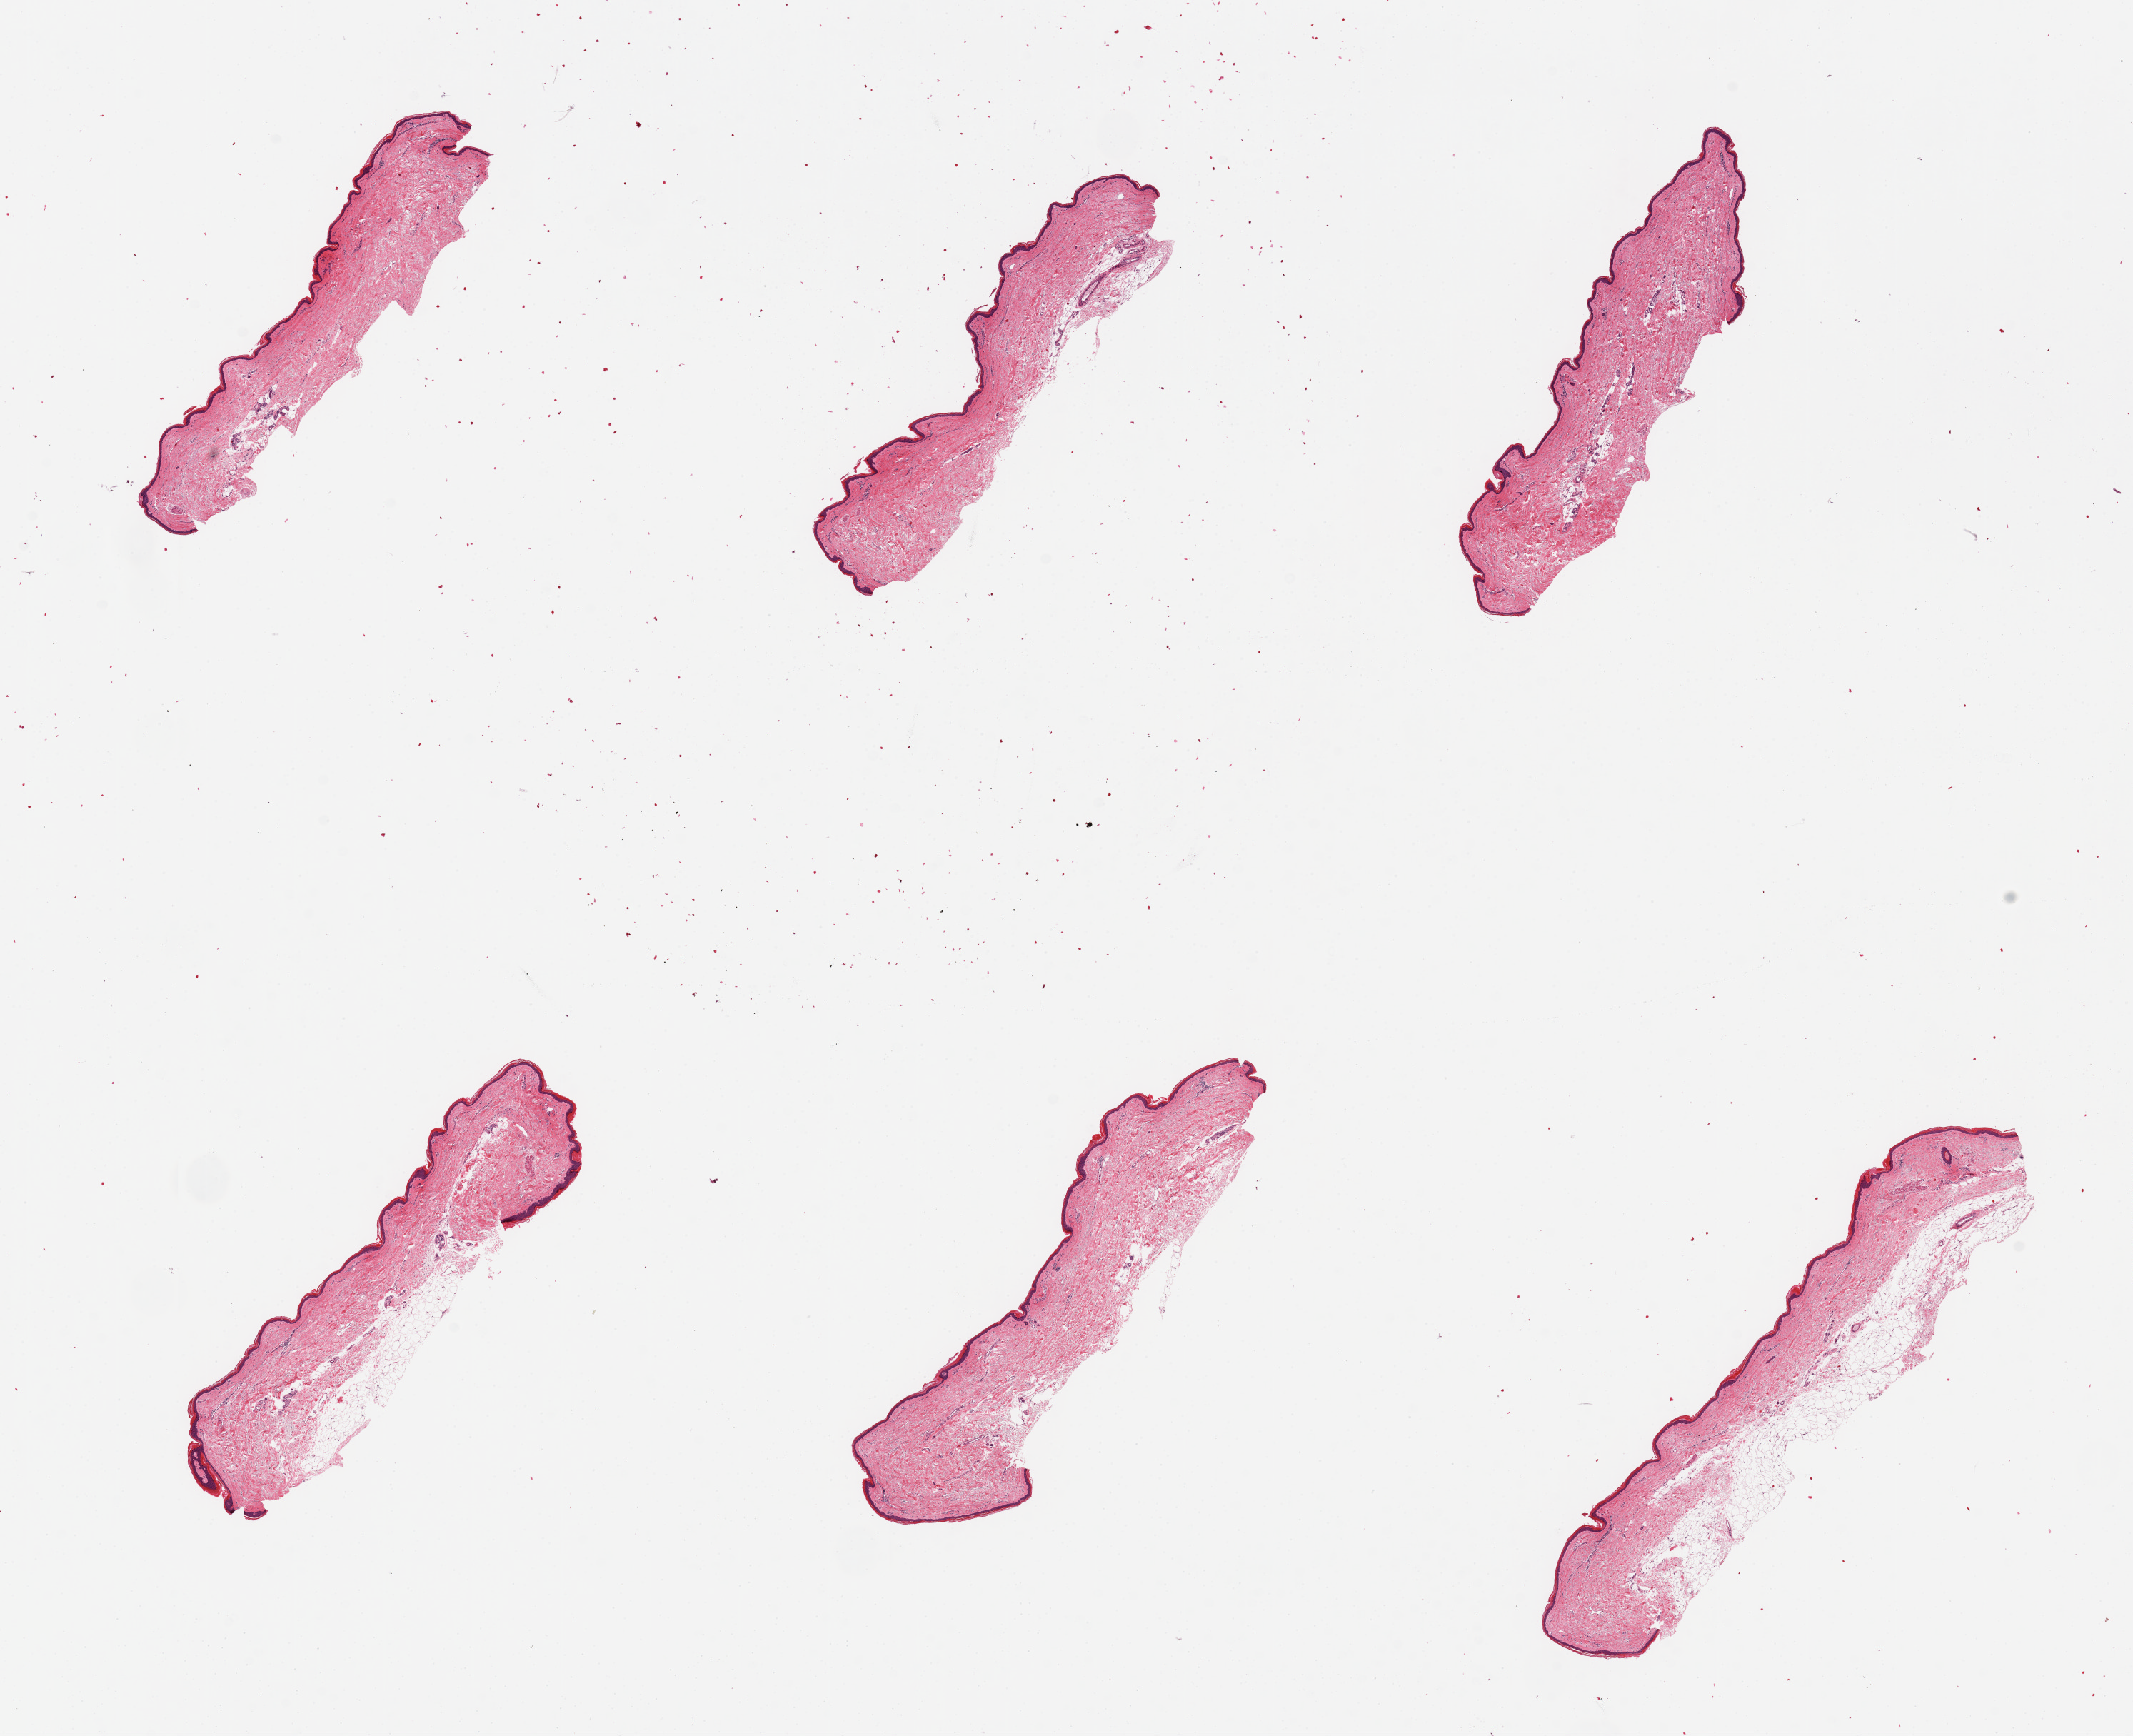
Digitized haematoxylin and eosin-stained section — whole scanned area (about 23.6 x 19.2 mm) shown as a low-resolution overview, PAXgene-fixed paraffin-embedded (PFPE) section, section of skin of lower leg (target tissue), donor tissue sample.
* reviewer comment on this tissue sample: 6 pieces, minimal fat